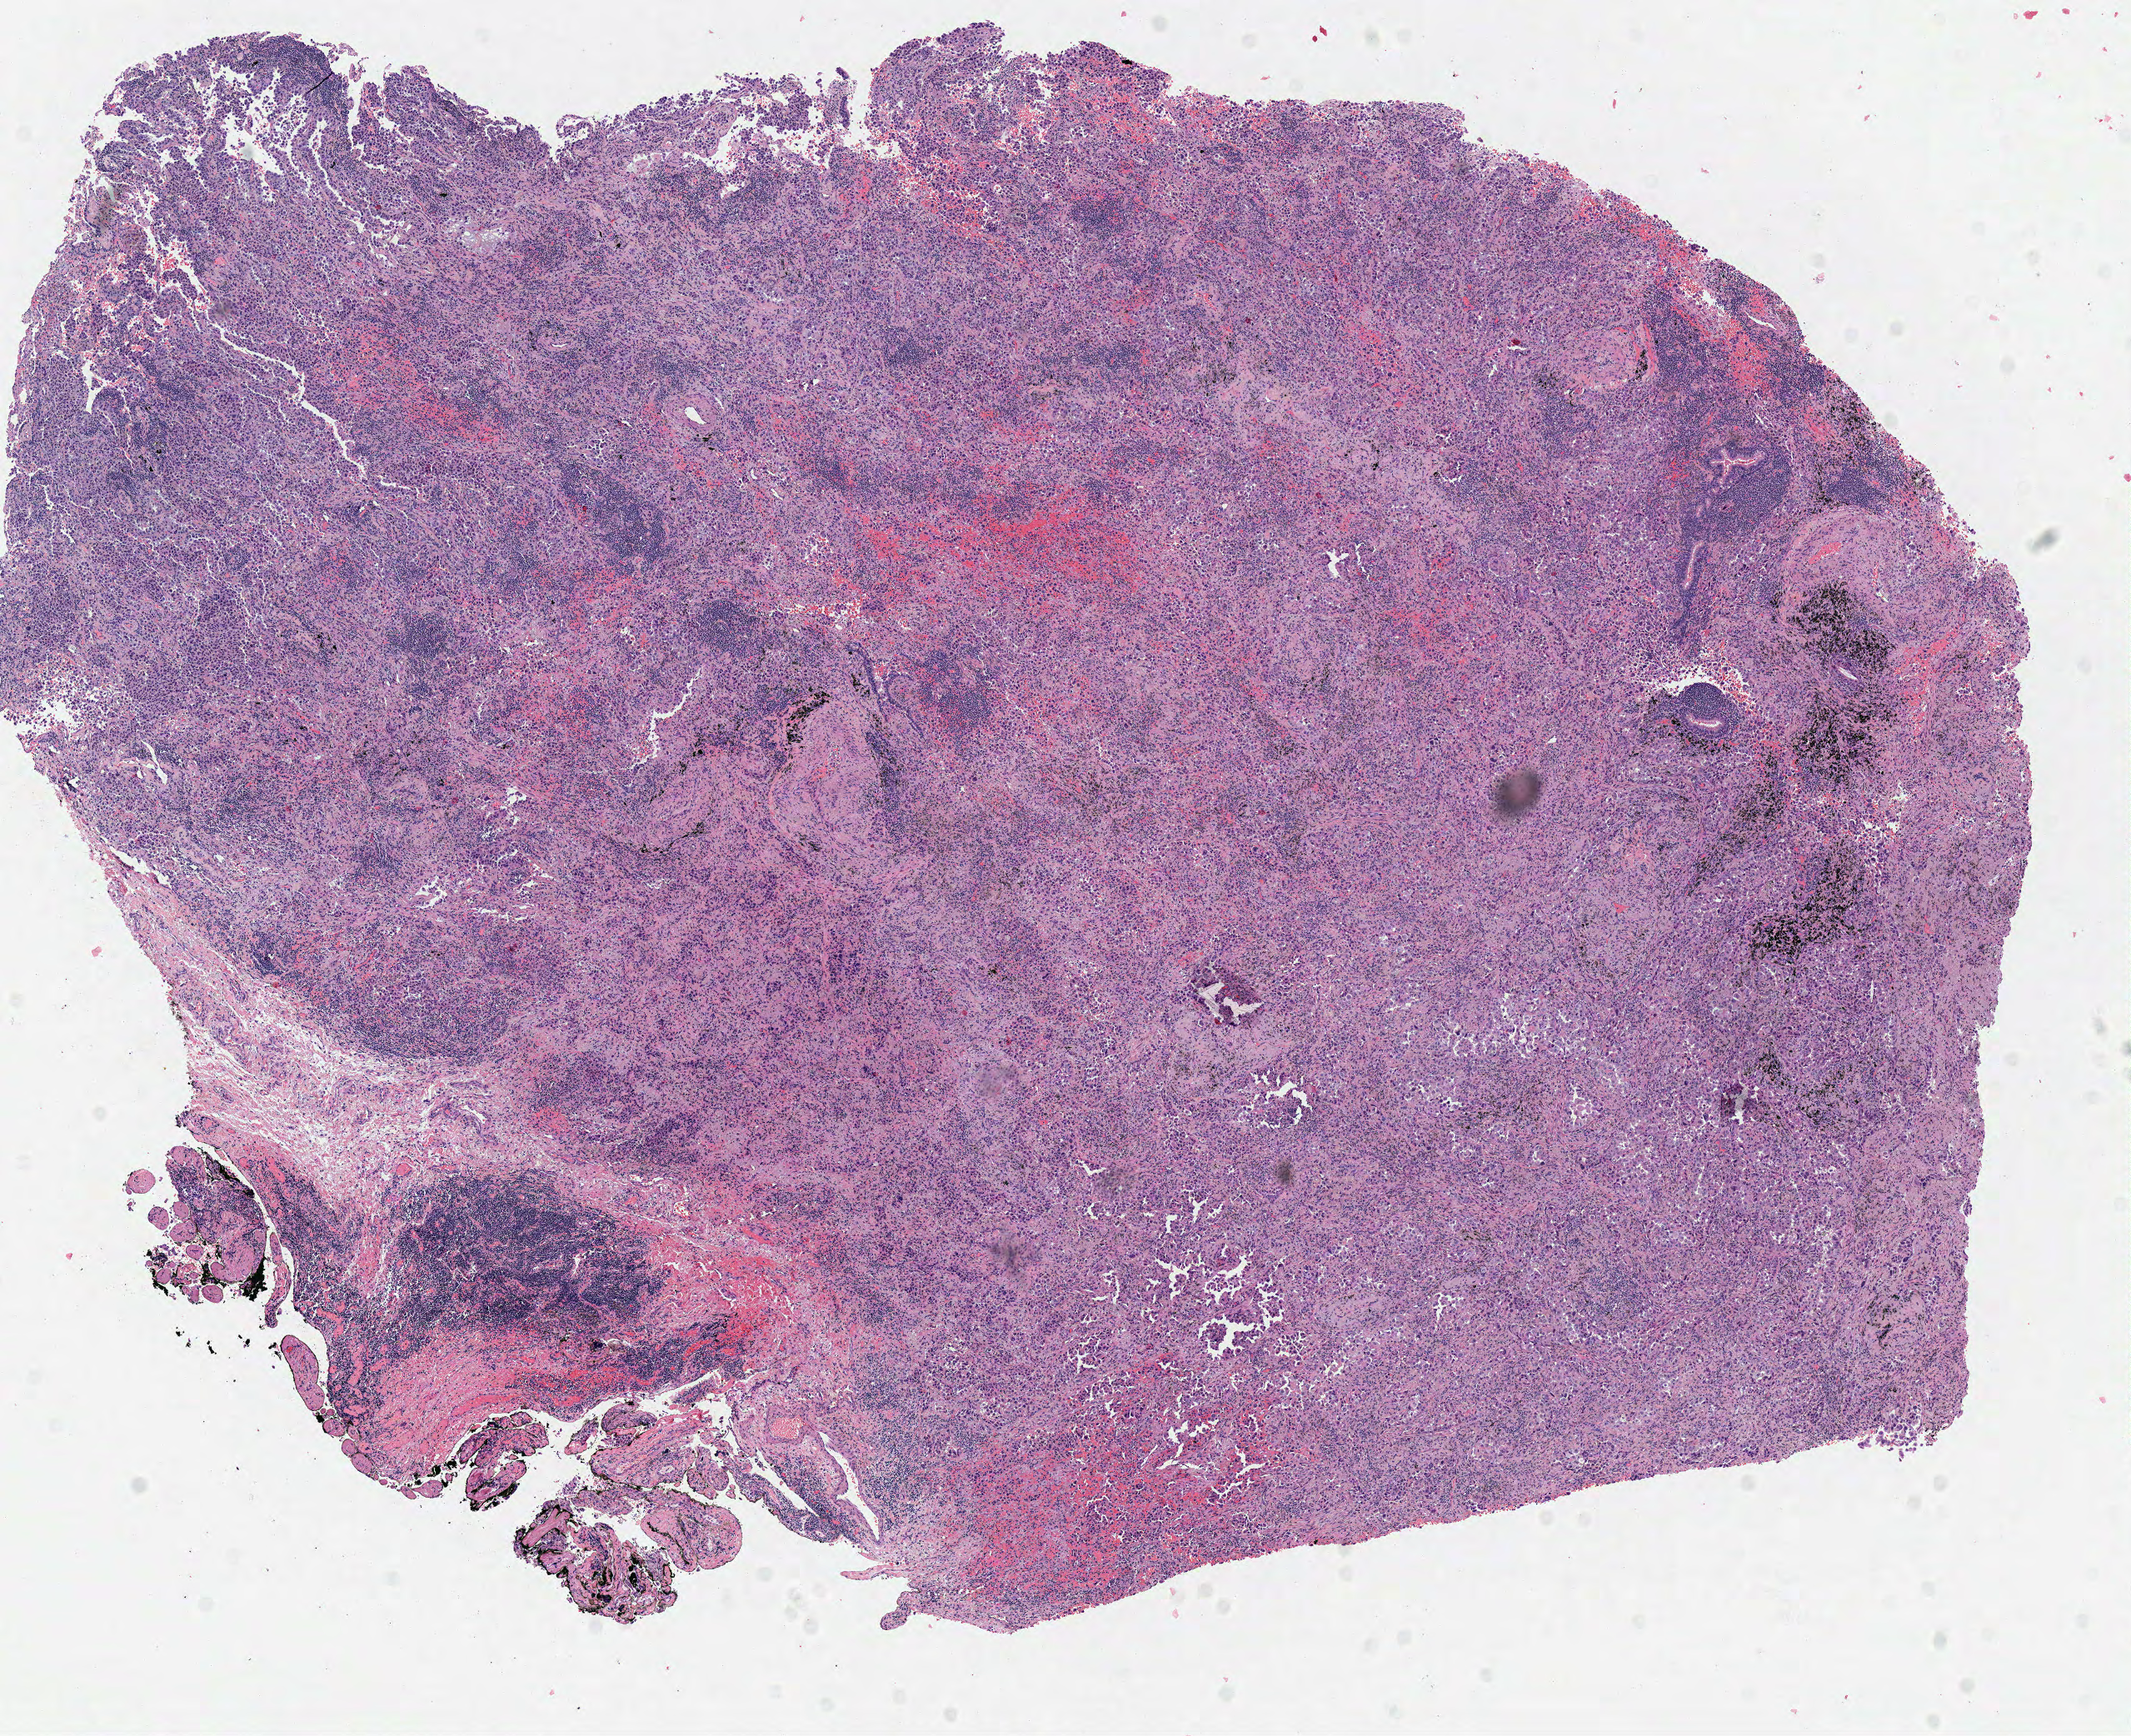
Whole-slide histology image, Hematoxylin and eosin (H&E) stained — shown as a low-resolution overview of the whole scanned area (about 10.1 x 8.2 mm, acquisition: 40x scan). Frozen section from the top of the tissue portion. Primary tumour sample from the lung. Patient: female, age at initial diagnosis 81 years. Composition of this section per pathologist review: tumour cells 95%, tumour nuclei 65%, normal cells 0%, stromal cells 5%, necrosis 0%.
AJCC pathologic stage: IA (7th edition). TNM: T1 N0 M0. Histologic diagnosis: Adenocarcinoma, NOS.